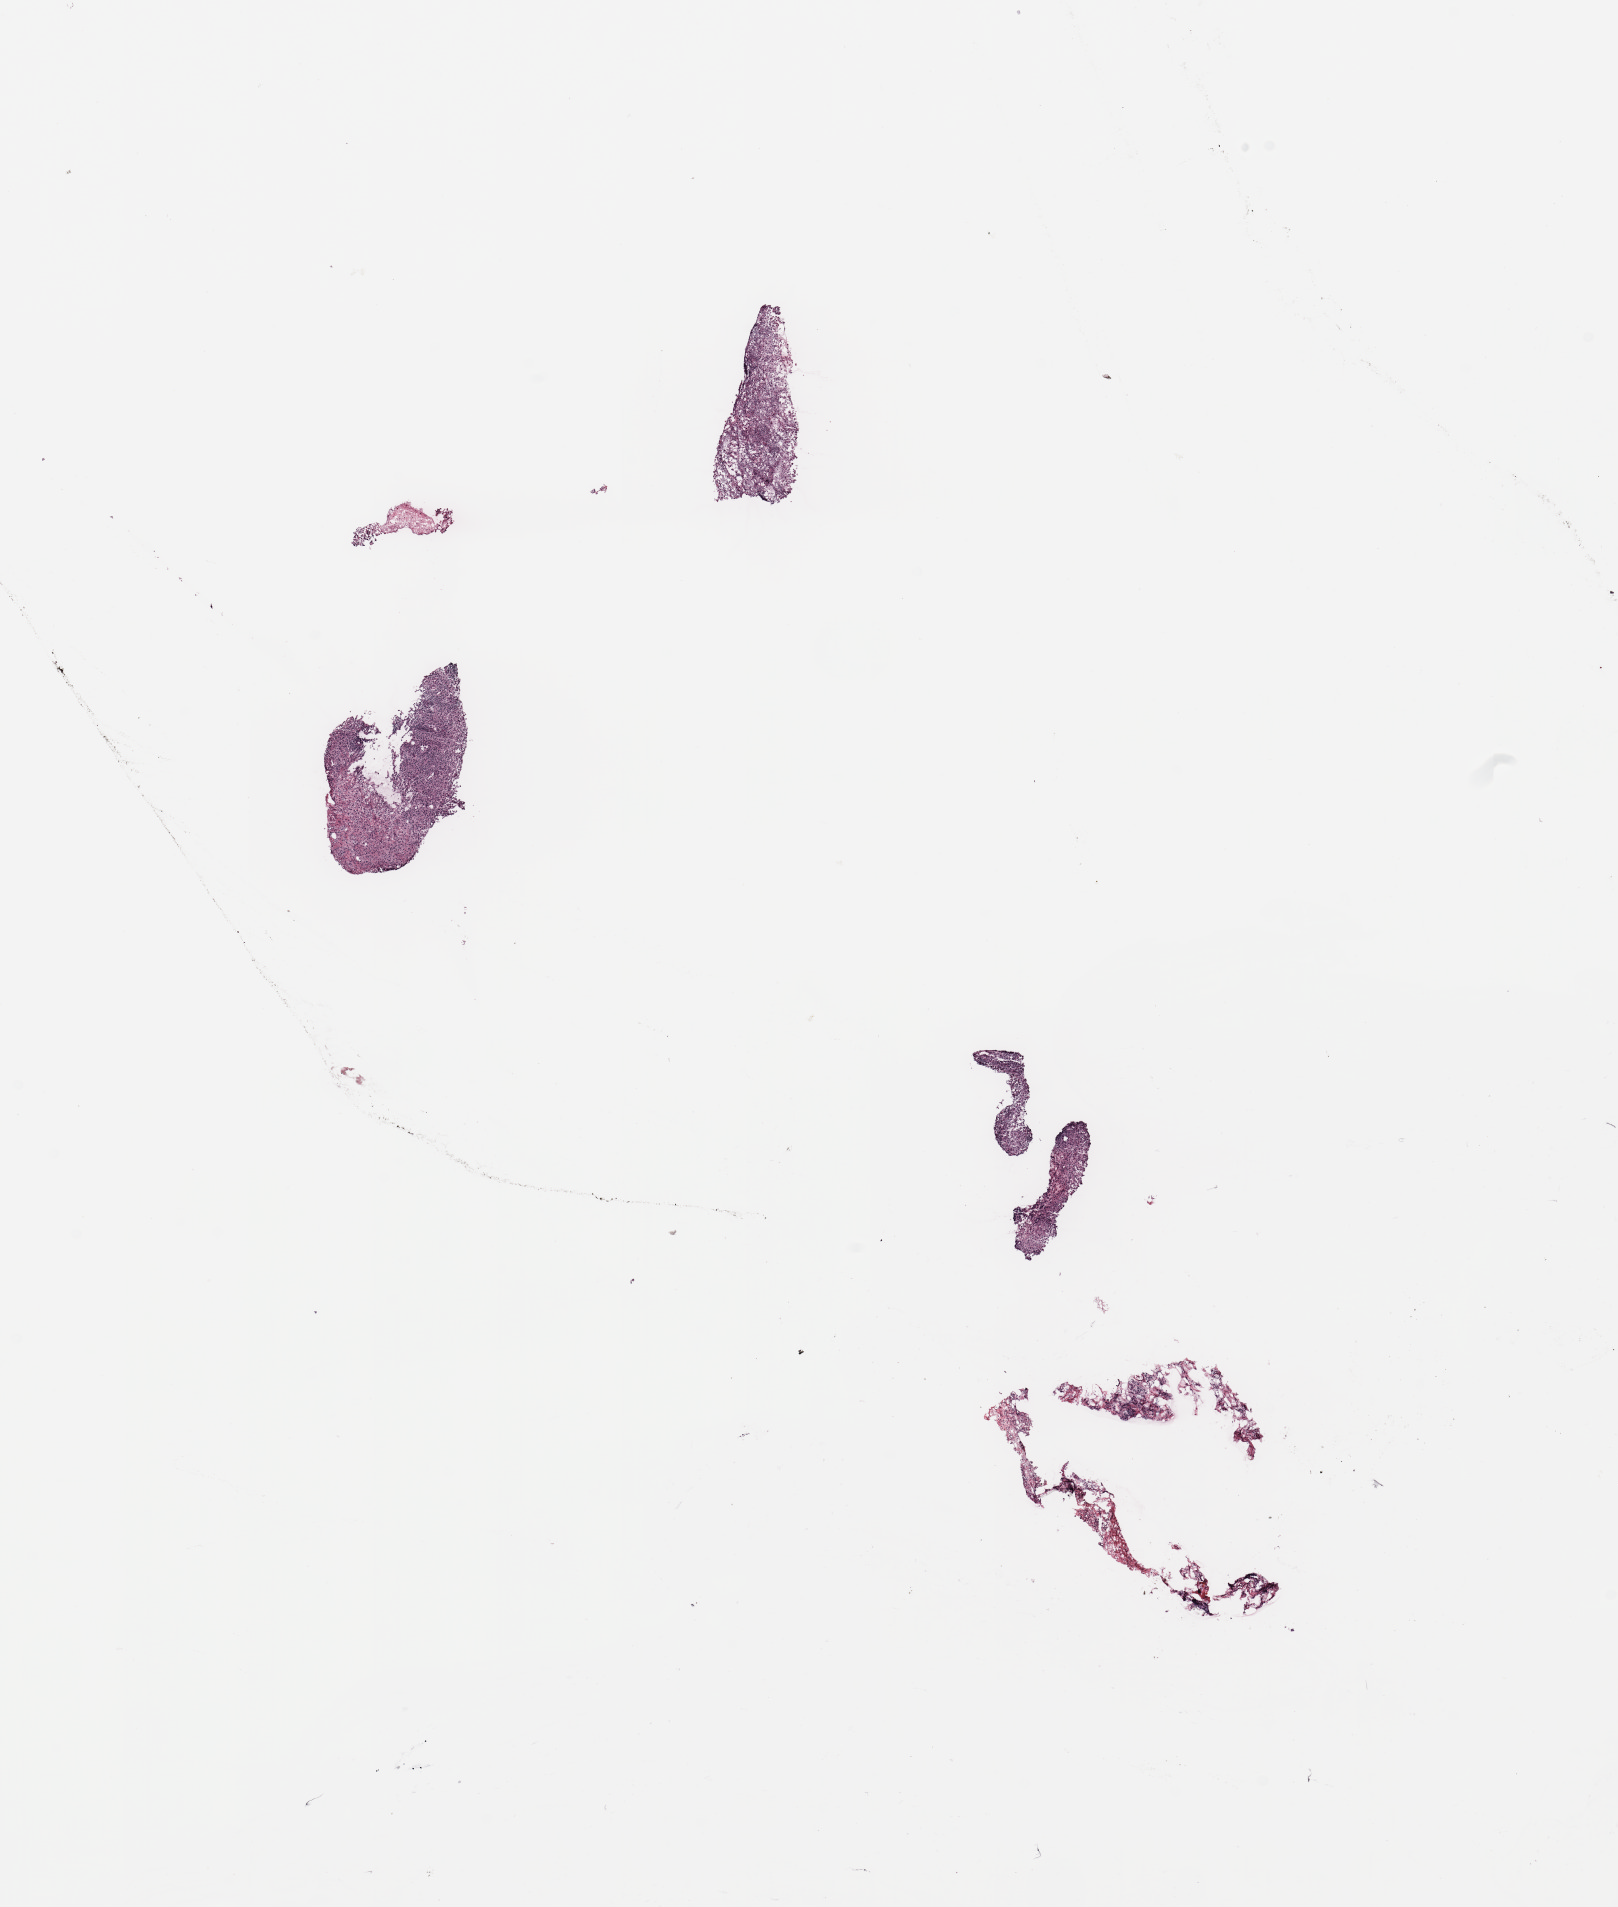
Whole-slide histology image, H&E-stained — shown as a low-resolution overview of the whole scanned area (about 12.8 x 15.1 mm, slide scanned at 20x), tumour tissue sample, breast. Female, 59 y/o.
Diagnosis: Adenocarcinoma, NOS. AJCC pathologic stage: II.